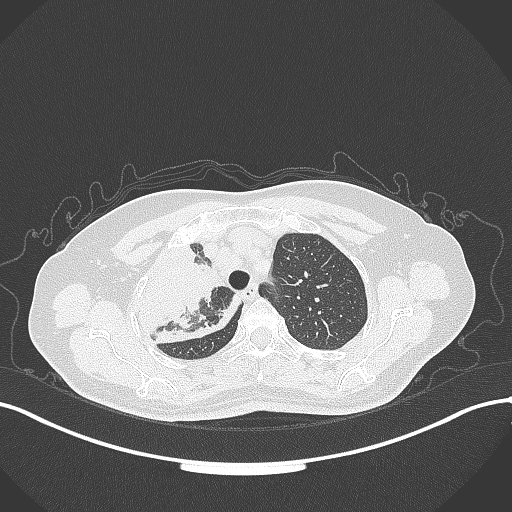
Chest CT, one axial slice; position 251 of 309 along the scan axis; reconstruction kernel B70f; lung window (W 1500 / L -600 HU); 1 mm slice thickness; 512 × 512 image matrix, field of view 400 × 400 mm. Female patient, age 60 years. Case-level facts recorded for this patient, not image findings: clinical TNM (as recorded): T3 N1 M1.
Annotated regions visible in this slice (rectangle marked by the reading radiologist):
- lung tumour (recorded histology: adenocarcinoma): bounding box <133,242,243,349> (left, top, right, bottom; pixels)